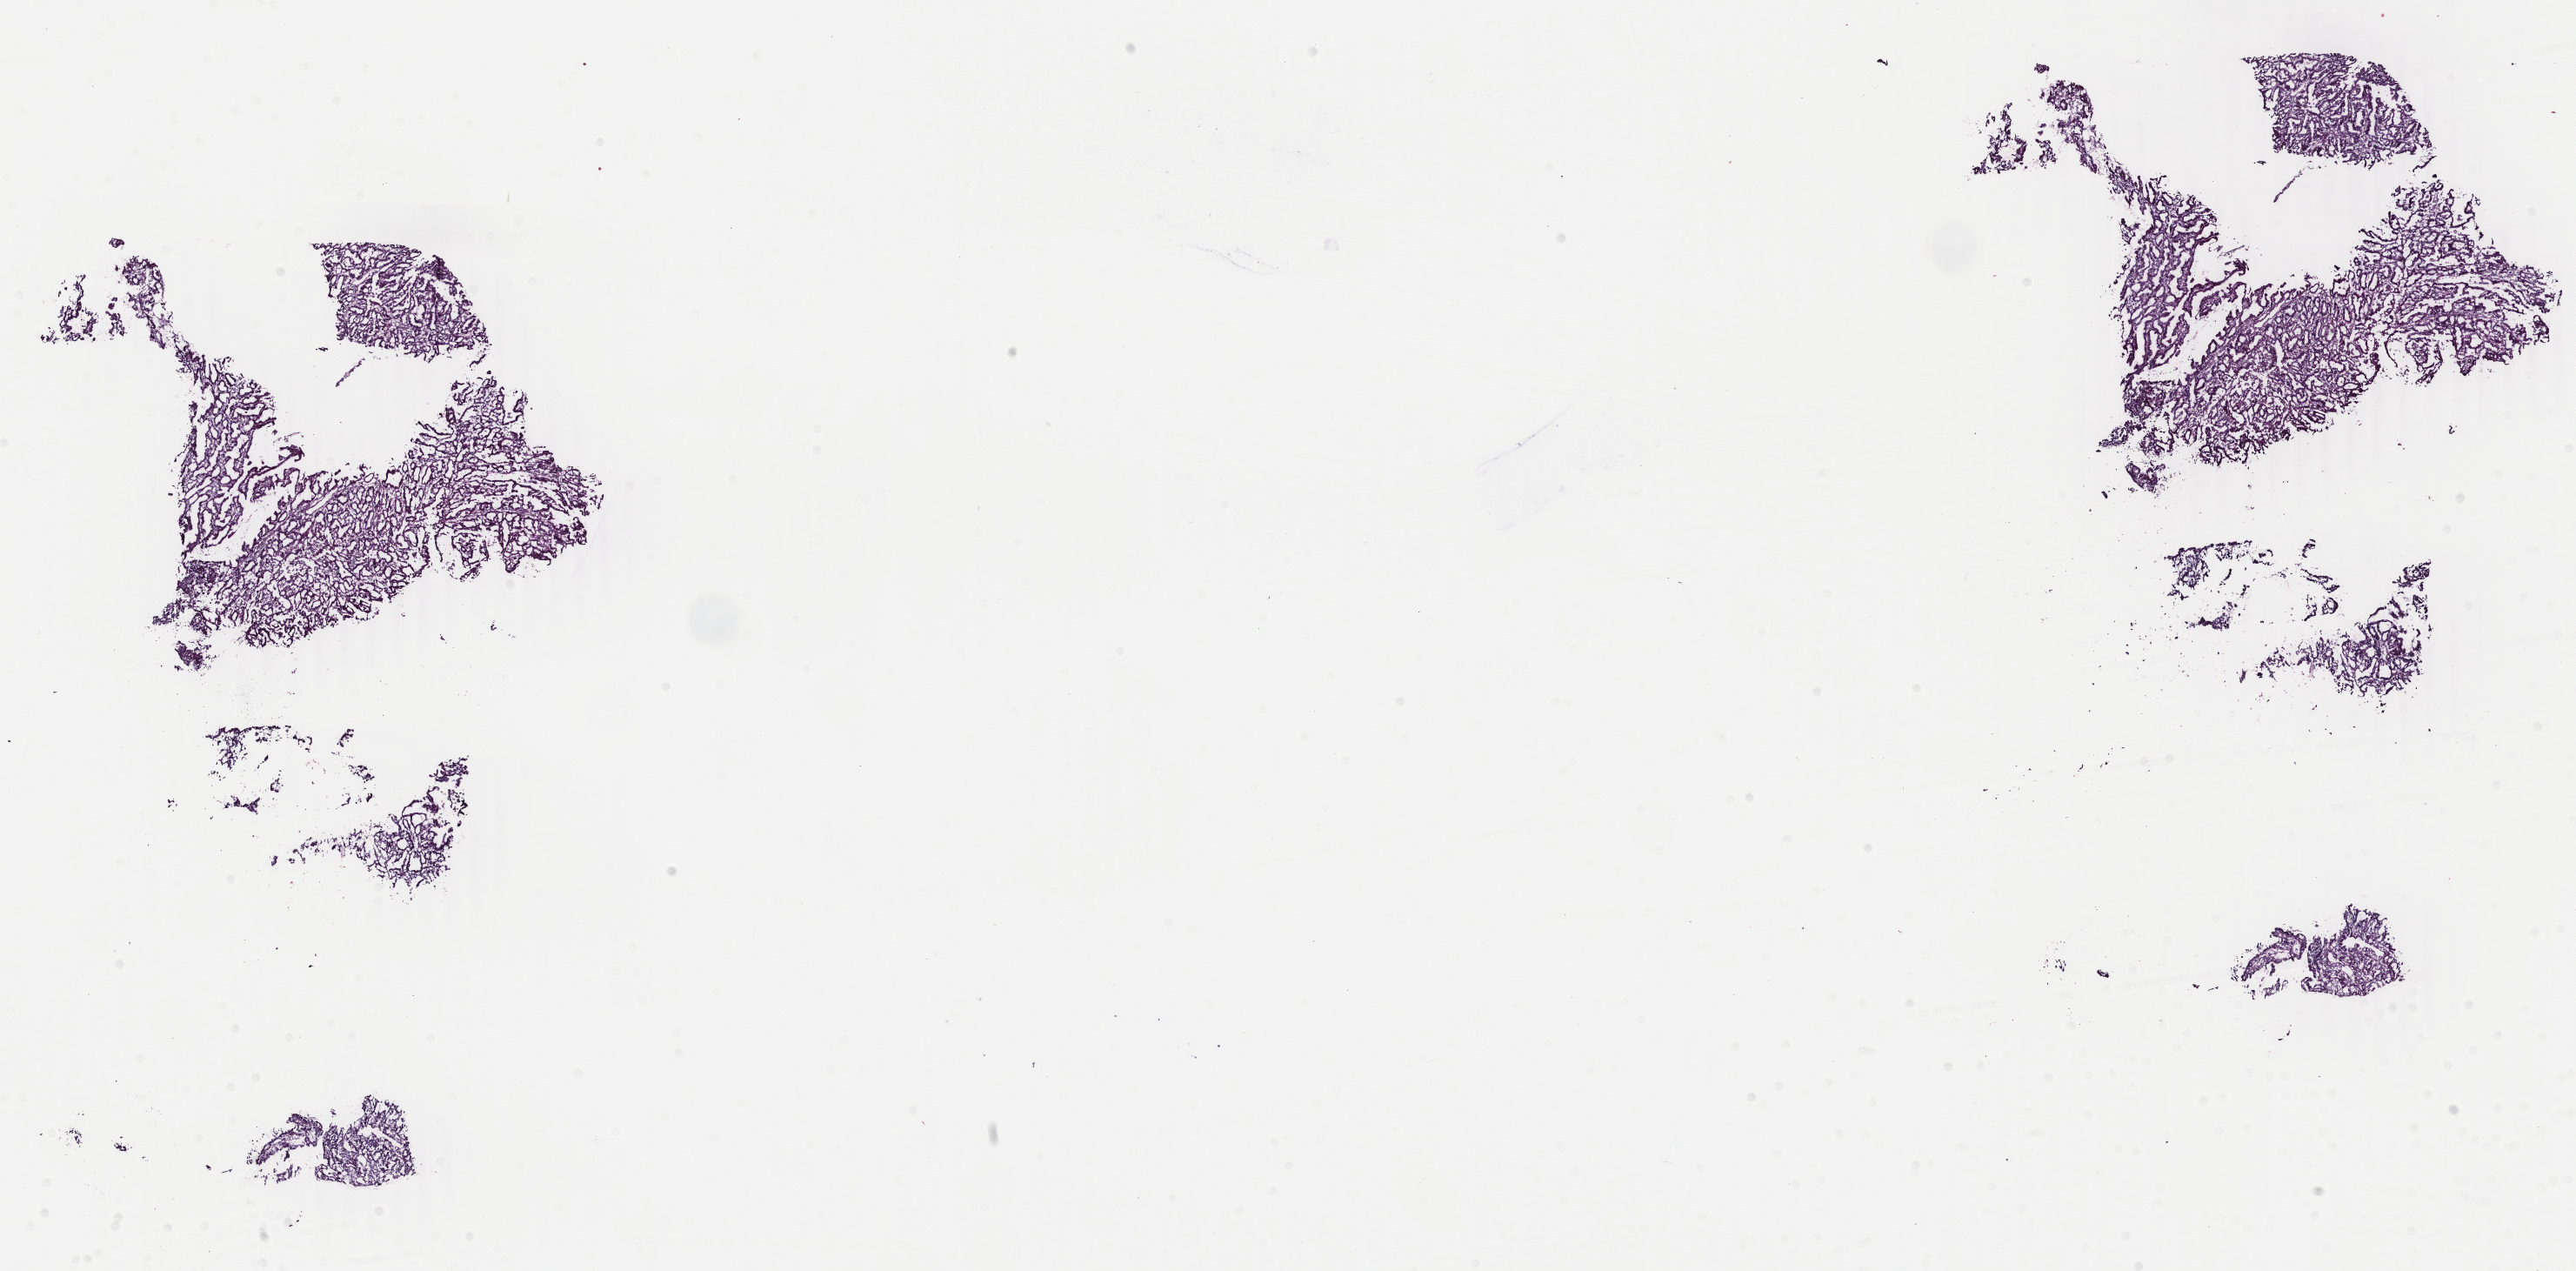
H&E-stained whole-slide image, whole scanned area (about 23.6 x 11.6 mm) shown as a low-resolution overview. Frozen section from the bottom of the tissue portion. Sample: primary tumour, uterus. Female patient; age at initial diagnosis 77 years. Histologic grade: G1 (well differentiated). Pathologist review of this section (percent, as recorded): tumour cells 60%, tumour nuclei 60%, normal cells 0%, stromal cells 40%, necrosis 0%. Inflammatory infiltration, as recorded: lymphocyte infiltration 40%, monocyte infiltration 20%, neutrophil infiltration 30%.
FIGO stage: IA. Pathologic diagnosis: Endometrioid adenocarcinoma, NOS (endometrium).